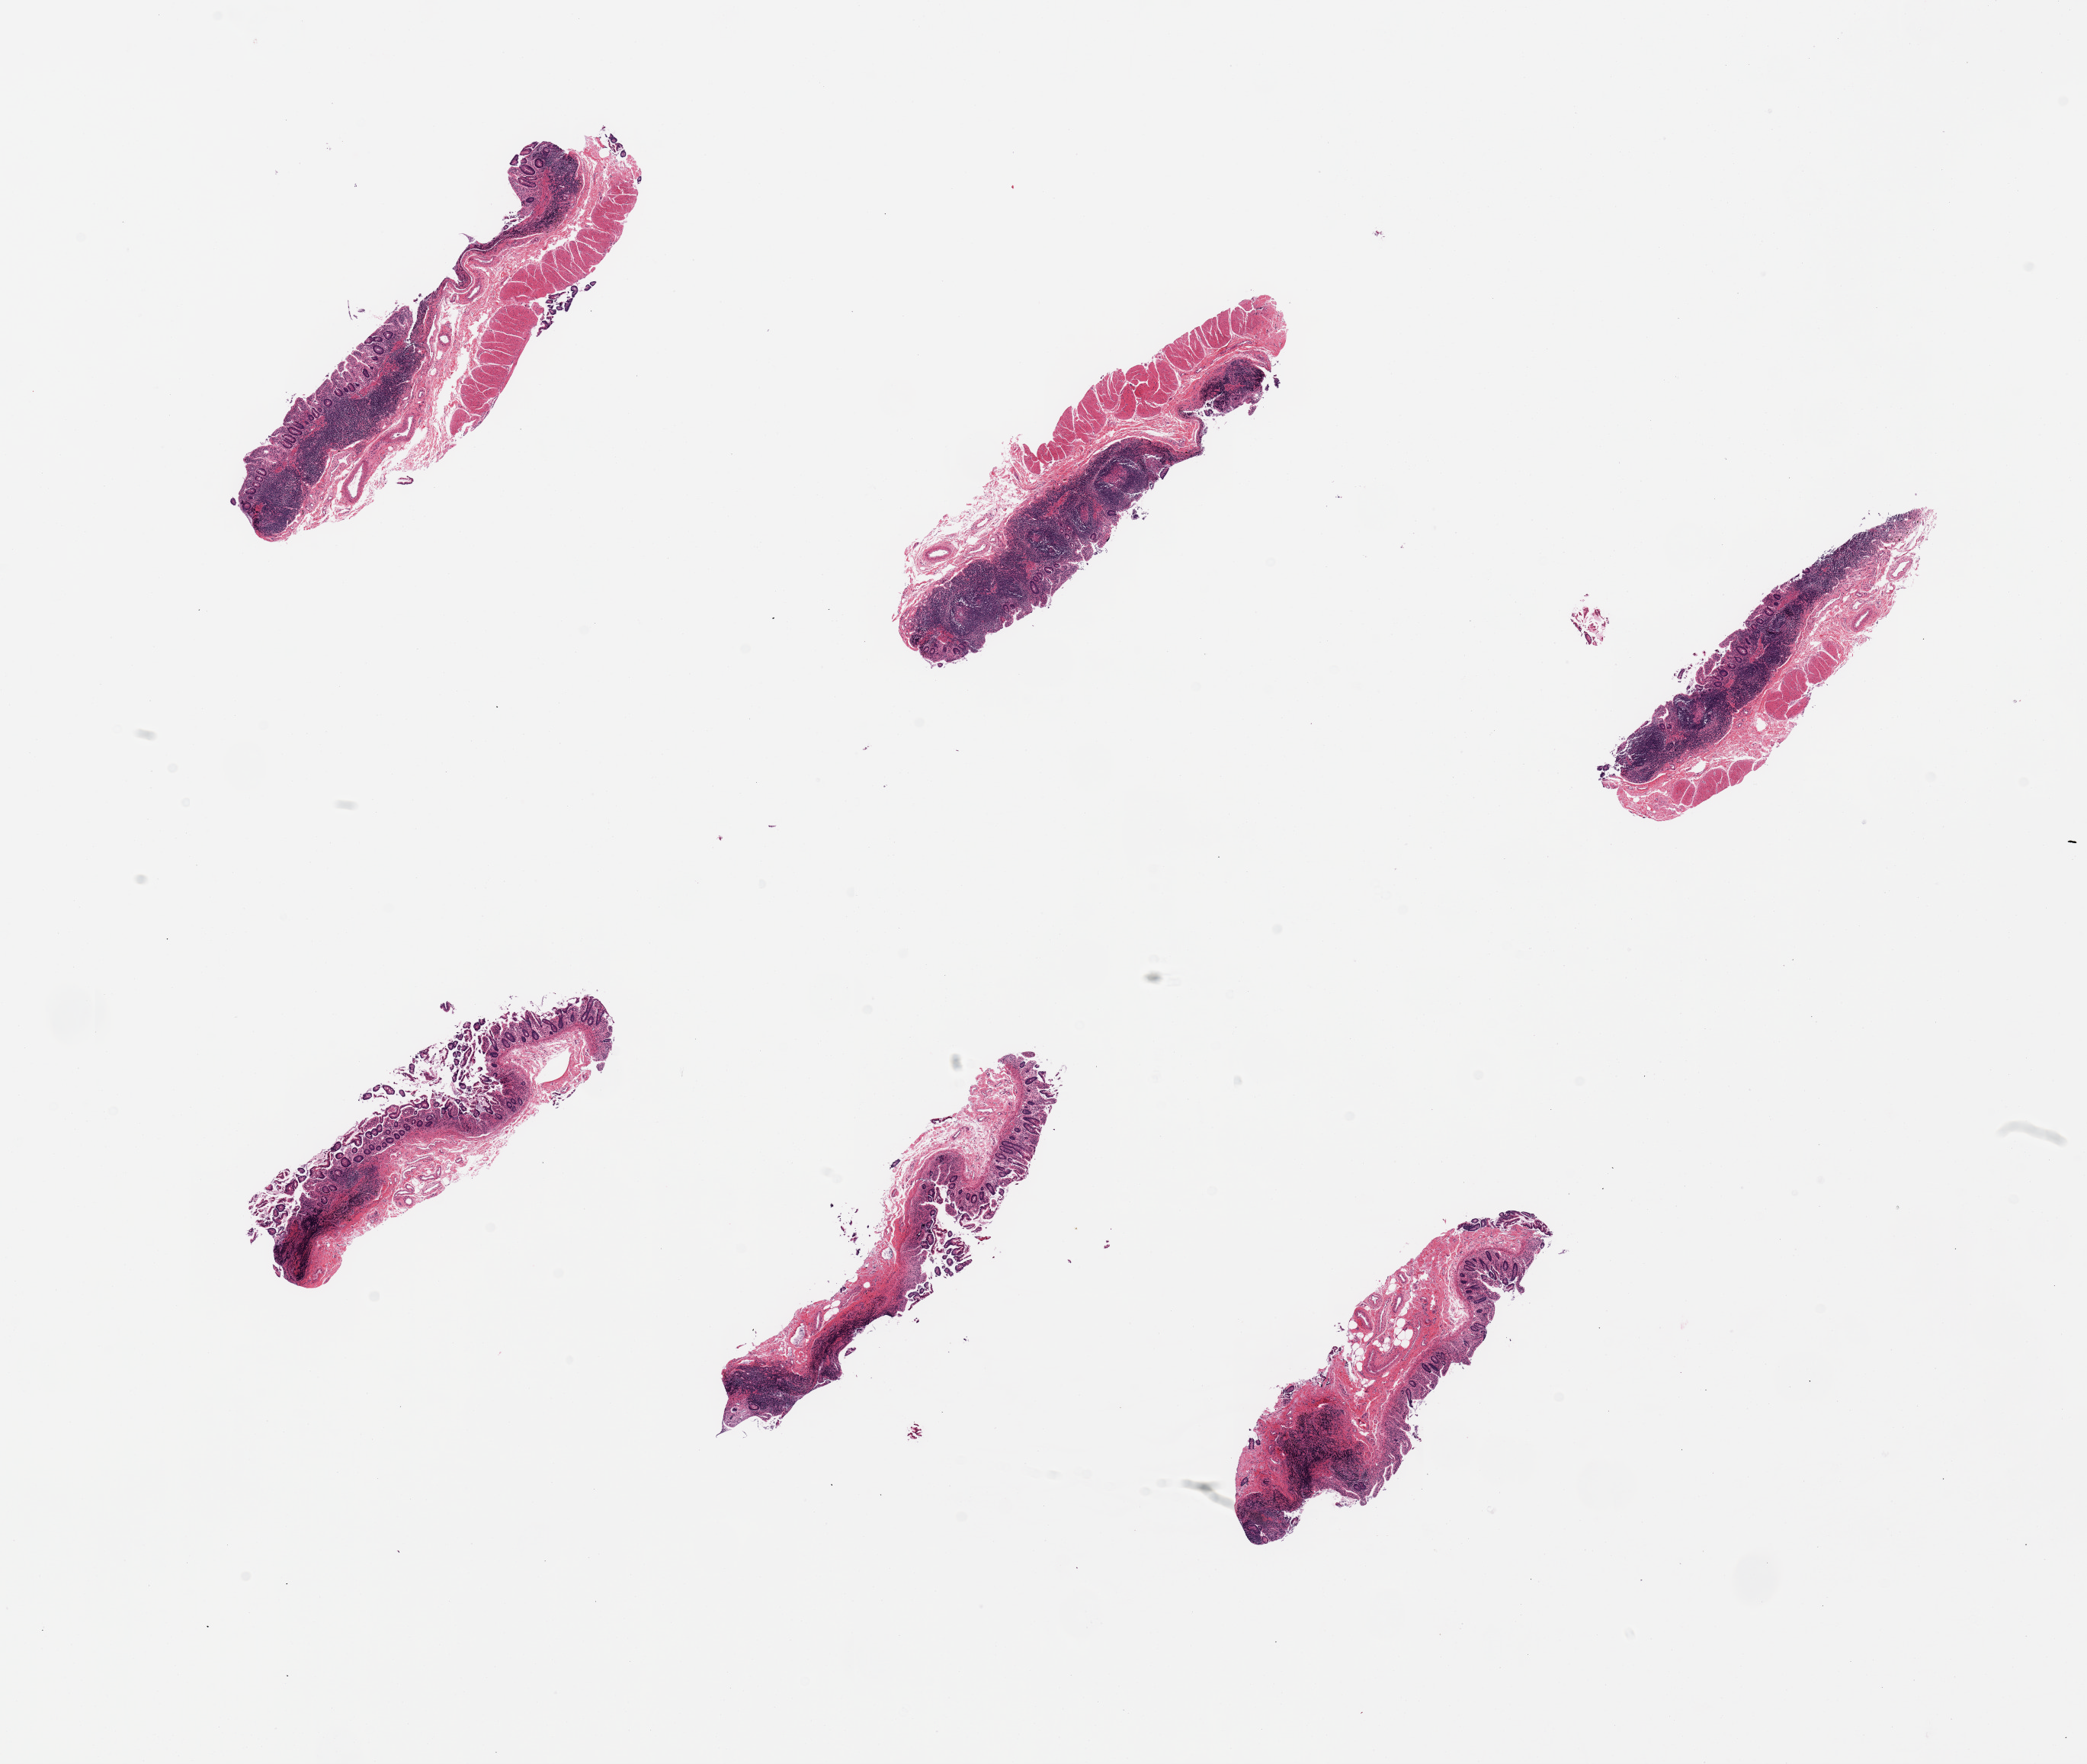
Hematoxylin and eosin (H&E) whole-slide image, shown as a low-resolution overview of the whole scanned area (about 21.7 x 18.3 mm, from a 20x scan); PAXgene-fixed paraffin-embedded (PFPE) section; sampled site (target tissue): ileum; donor tissue sample.
Pathologist's review note for this sample: 6 pieces, autolyzed mucosa, but with residual lymphoid tissue, muscularis (not target) also present.